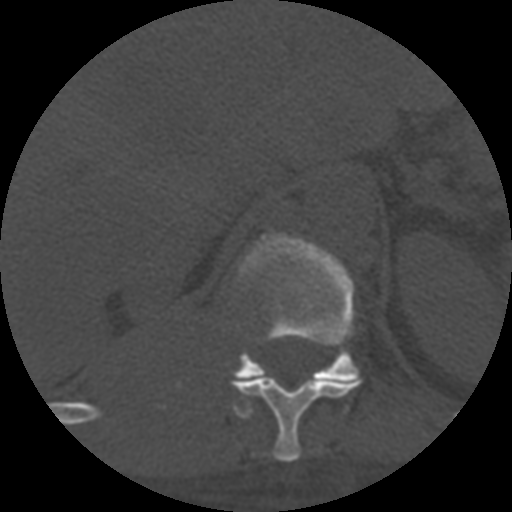
CT including the spine, one axial slice; position 325 of 708 along the scan axis; one of 3 acquisitions stored at this slice position; bone window (W 1800 / L 400 HU); 512 × 512 image matrix, field of view 160 × 160 mm. Patient age 55 years. From the clinical record (not read from this slice): primary cancer: colon.
Structures marked on this image (semi-automatic segmentation, software-assisted and operator-edited):
- T11 vertebra: bounding box [x1, y1, x2, y2] px = [231, 377, 359, 462]
- T12 vertebra: [233, 233, 360, 381]